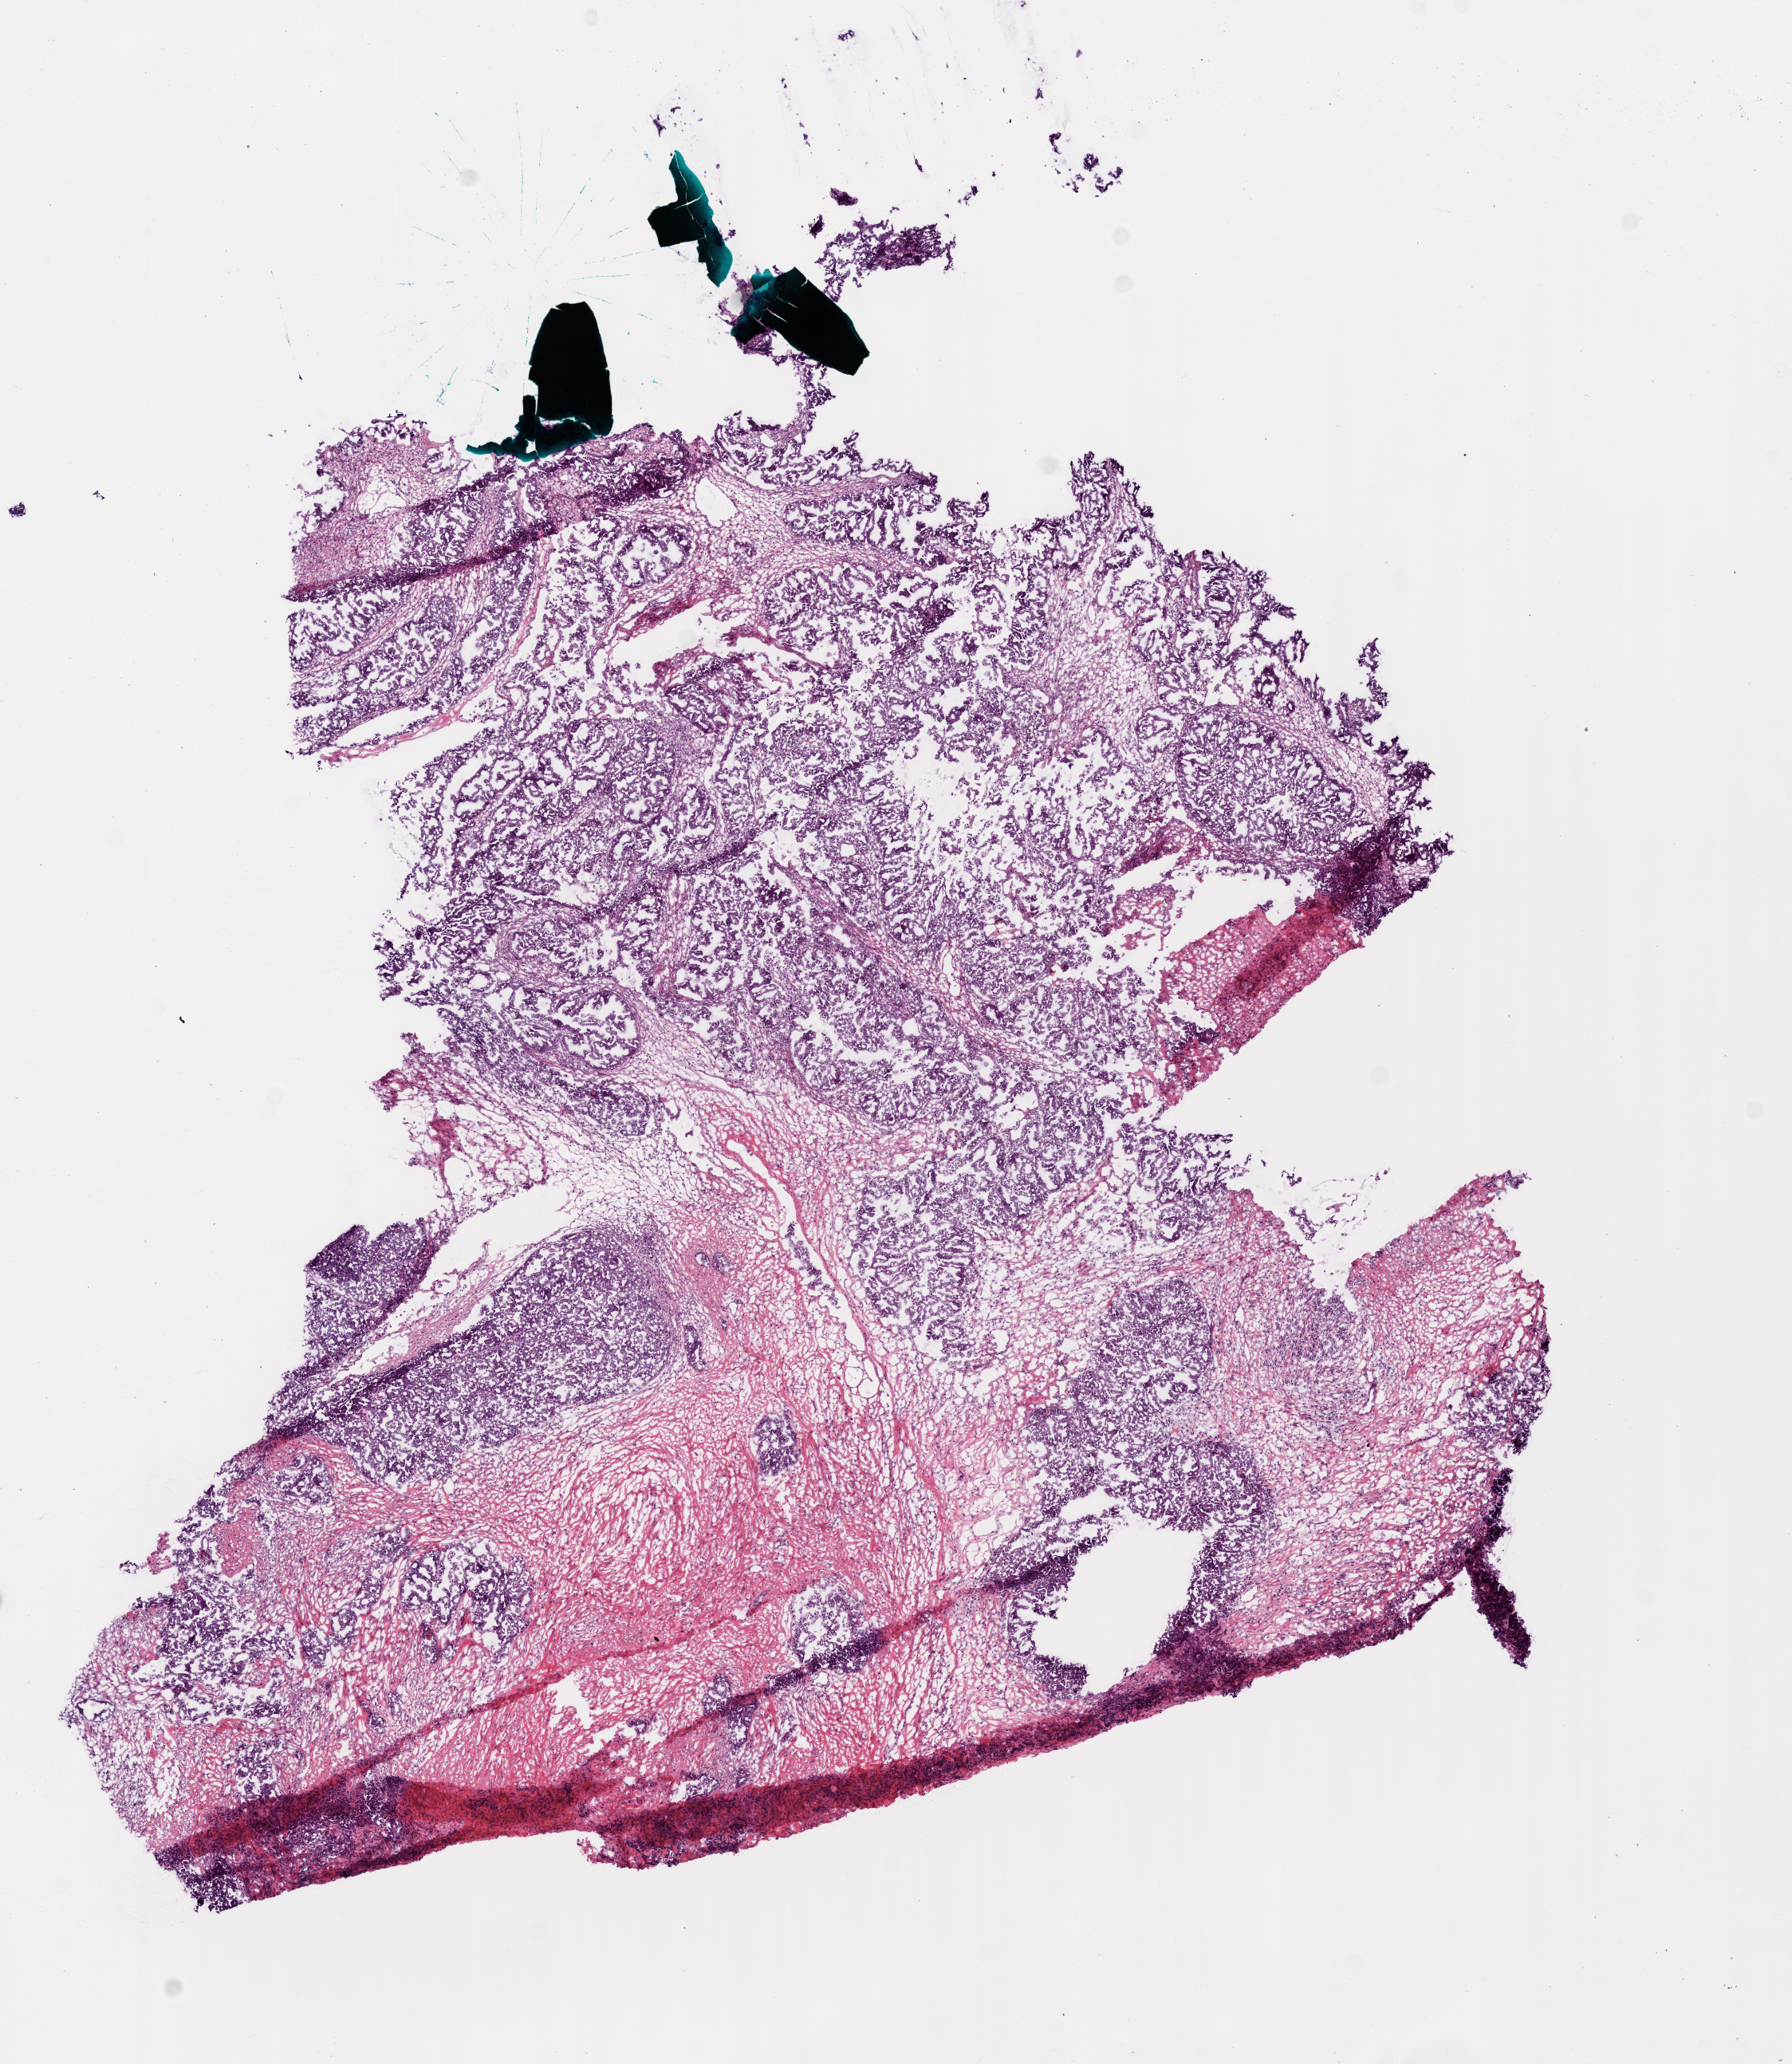
Digitized Hematoxylin and eosin (H&E) stained tissue section (whole slide), whole scanned area (about 9.0 x 10.4 mm) shown as a low-resolution overview. Frozen section. Primary tumour sample from the ovary. Female patient; age at initial diagnosis 64 years.
Pathologic diagnosis: Serous cystadenocarcinoma, NOS.